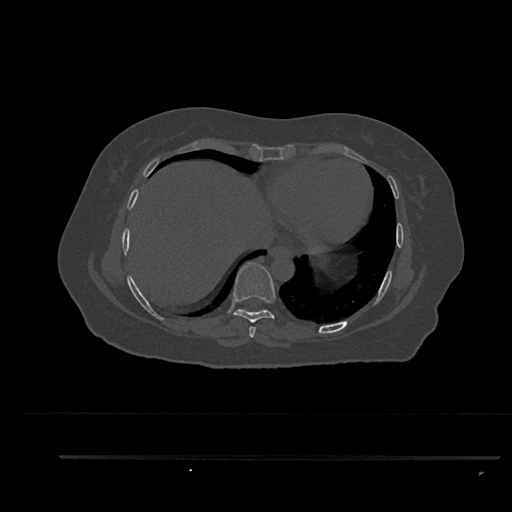
CT including the spine, one axial slice; slice 456 of 797 in the series (ordered by position); reconstruction kernel Br40s/3; 120 kVp; bone window (W 1800 / L 400 HU); 512 × 512 image matrix, field of view 408 × 408 mm. Female patient, age 44 years. From the clinical record (not read from this slice): primary cancer: renal.
Annotated regions visible in this slice (semi-automatically segmented with operator editing):
- T7 vertebra: bounding box (x1, y1, x2, y2) in pixels: (249, 326, 256, 338)
- T8 vertebra: (233, 262, 276, 323)